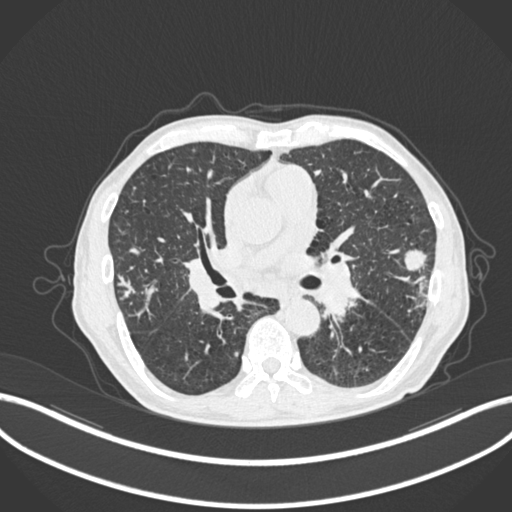
Chest CT, one axial slice; reconstruction kernel B30f; 120 kVp; lung window (W 1500 / L -600 HU); 512 × 512 image matrix, field of view 400 × 400 mm. Patient: male, 74 years. From the clinical record (not read from this slice): clinical TNM (as recorded): T2a N1 M0.
Outlined on this slice (bounding box drawn by a radiologist):
- lung tumour (recorded histology: adenocarcinoma): box from (x=403, y=246) to (x=432, y=272) px